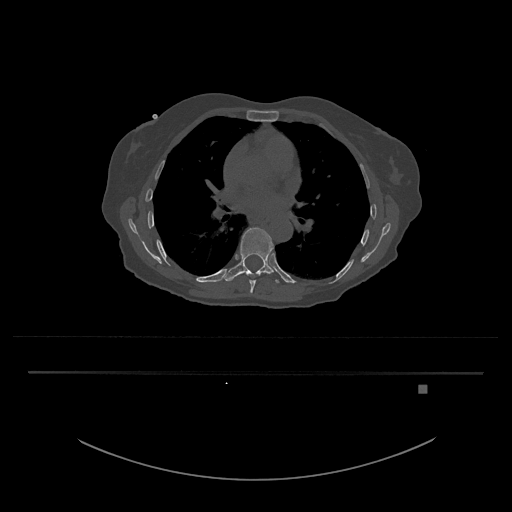
CT including the spine, one axial slice; position 774 of 797 along the scan axis; reconstruction kernel Br40s/3; bone window (W 1800 / L 400 HU); 0.5 mm slice thickness; 512 × 512 image matrix, field of view 500 × 500 mm. Female patient, age 57 years. From the clinical record (not read from this slice): primary cancer: cervical.
Outlined on this slice (semi-automatically segmented with operator editing):
- T8 vertebra: box from (x=246, y=272) to (x=263, y=293) px
- T9 vertebra: (x=224, y=227)–(x=280, y=284)